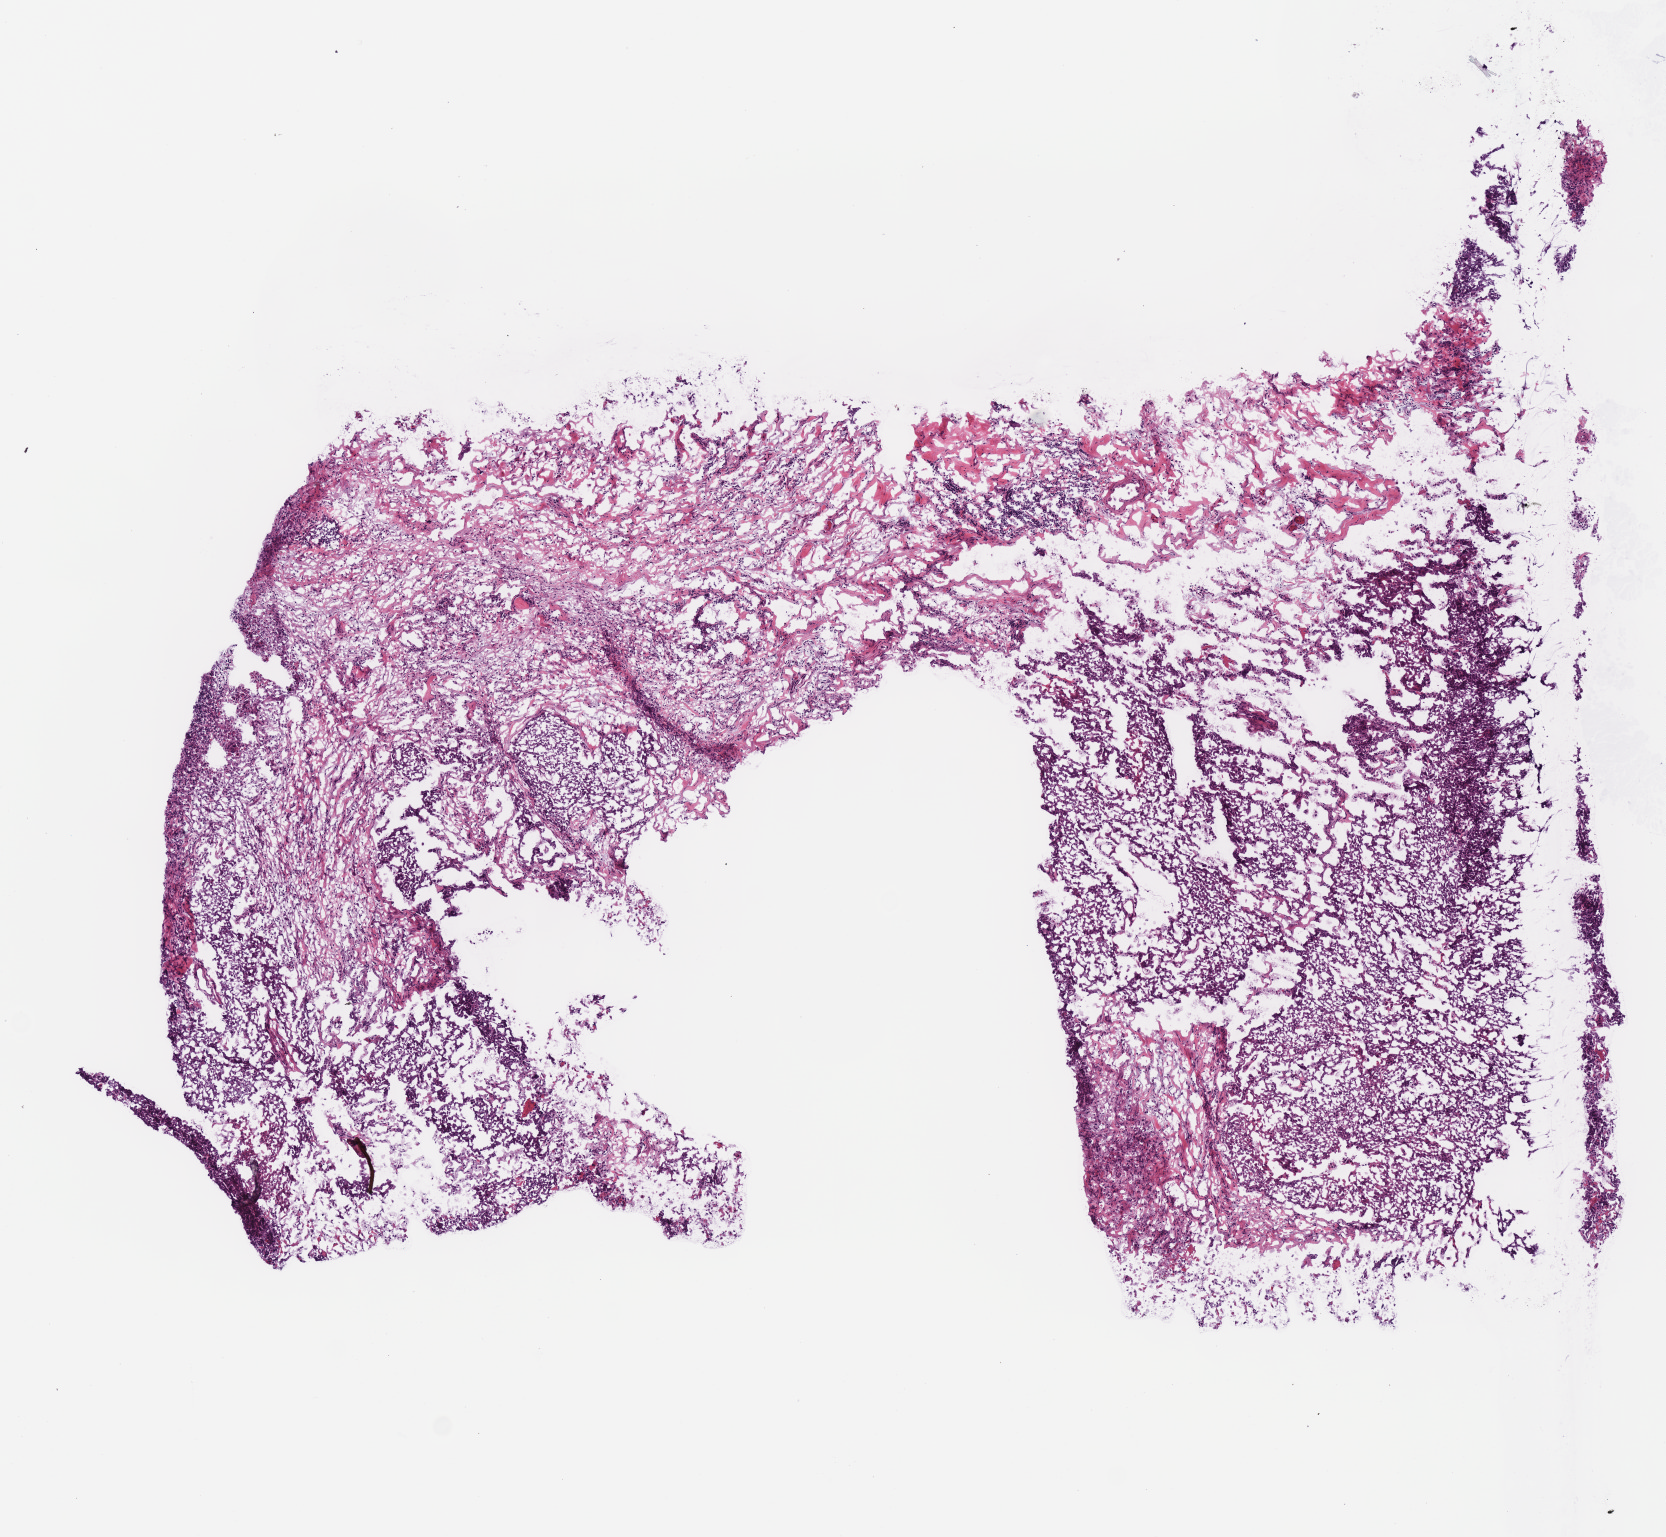
Whole-slide histology image, H&E-stained — whole scanned area (about 6.6 x 6.1 mm) shown as a low-resolution overview, frozen section from the top of the tissue portion, primary tumour sample from the head and neck. Male patient; age at initial diagnosis 62 years. Histologic grade: G2 (moderately differentiated). Pathologist review of this section (percent, as recorded): tumour cells 75%, tumour nuclei 65%, normal cells 0%, stromal cells 25%, necrosis 0%. Infiltration values recorded for this section: lymphocyte infiltration 20%, monocyte infiltration 0%, neutrophil infiltration 0%.
AJCC pathologic stage: IVA (7th edition). Diagnosis: Squamous cell carcinoma, NOS (larynx, NOS). Laterality: left. TNM: T4a N2b.